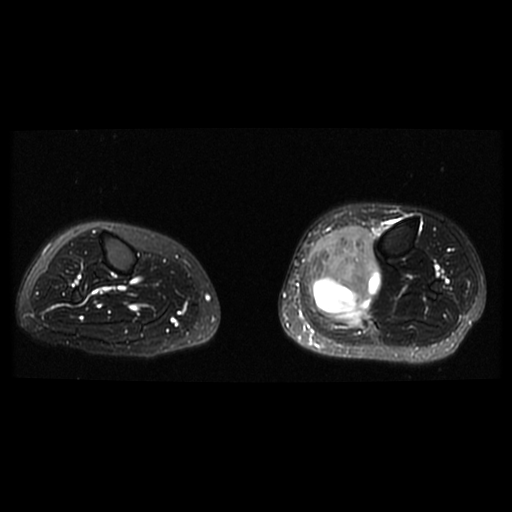
MRI of an extremity soft-tissue mass, one axial slice; position 14 of 38 along the scan axis; T2-weighted fat-saturated; 6 mm slice thickness; 512 × 512 image matrix. Female patient. Case-level facts recorded for this patient, not image findings: histological type: extraskeletal high grade osteogenic sarcoma; grade: high; site of the primary tumour: left calf.
Outlined on this slice (outlined manually by an expert reader):
- gross tumour volume (mass): bounding box (x1, y1, x2, y2) in pixels: (308, 226, 381, 319)